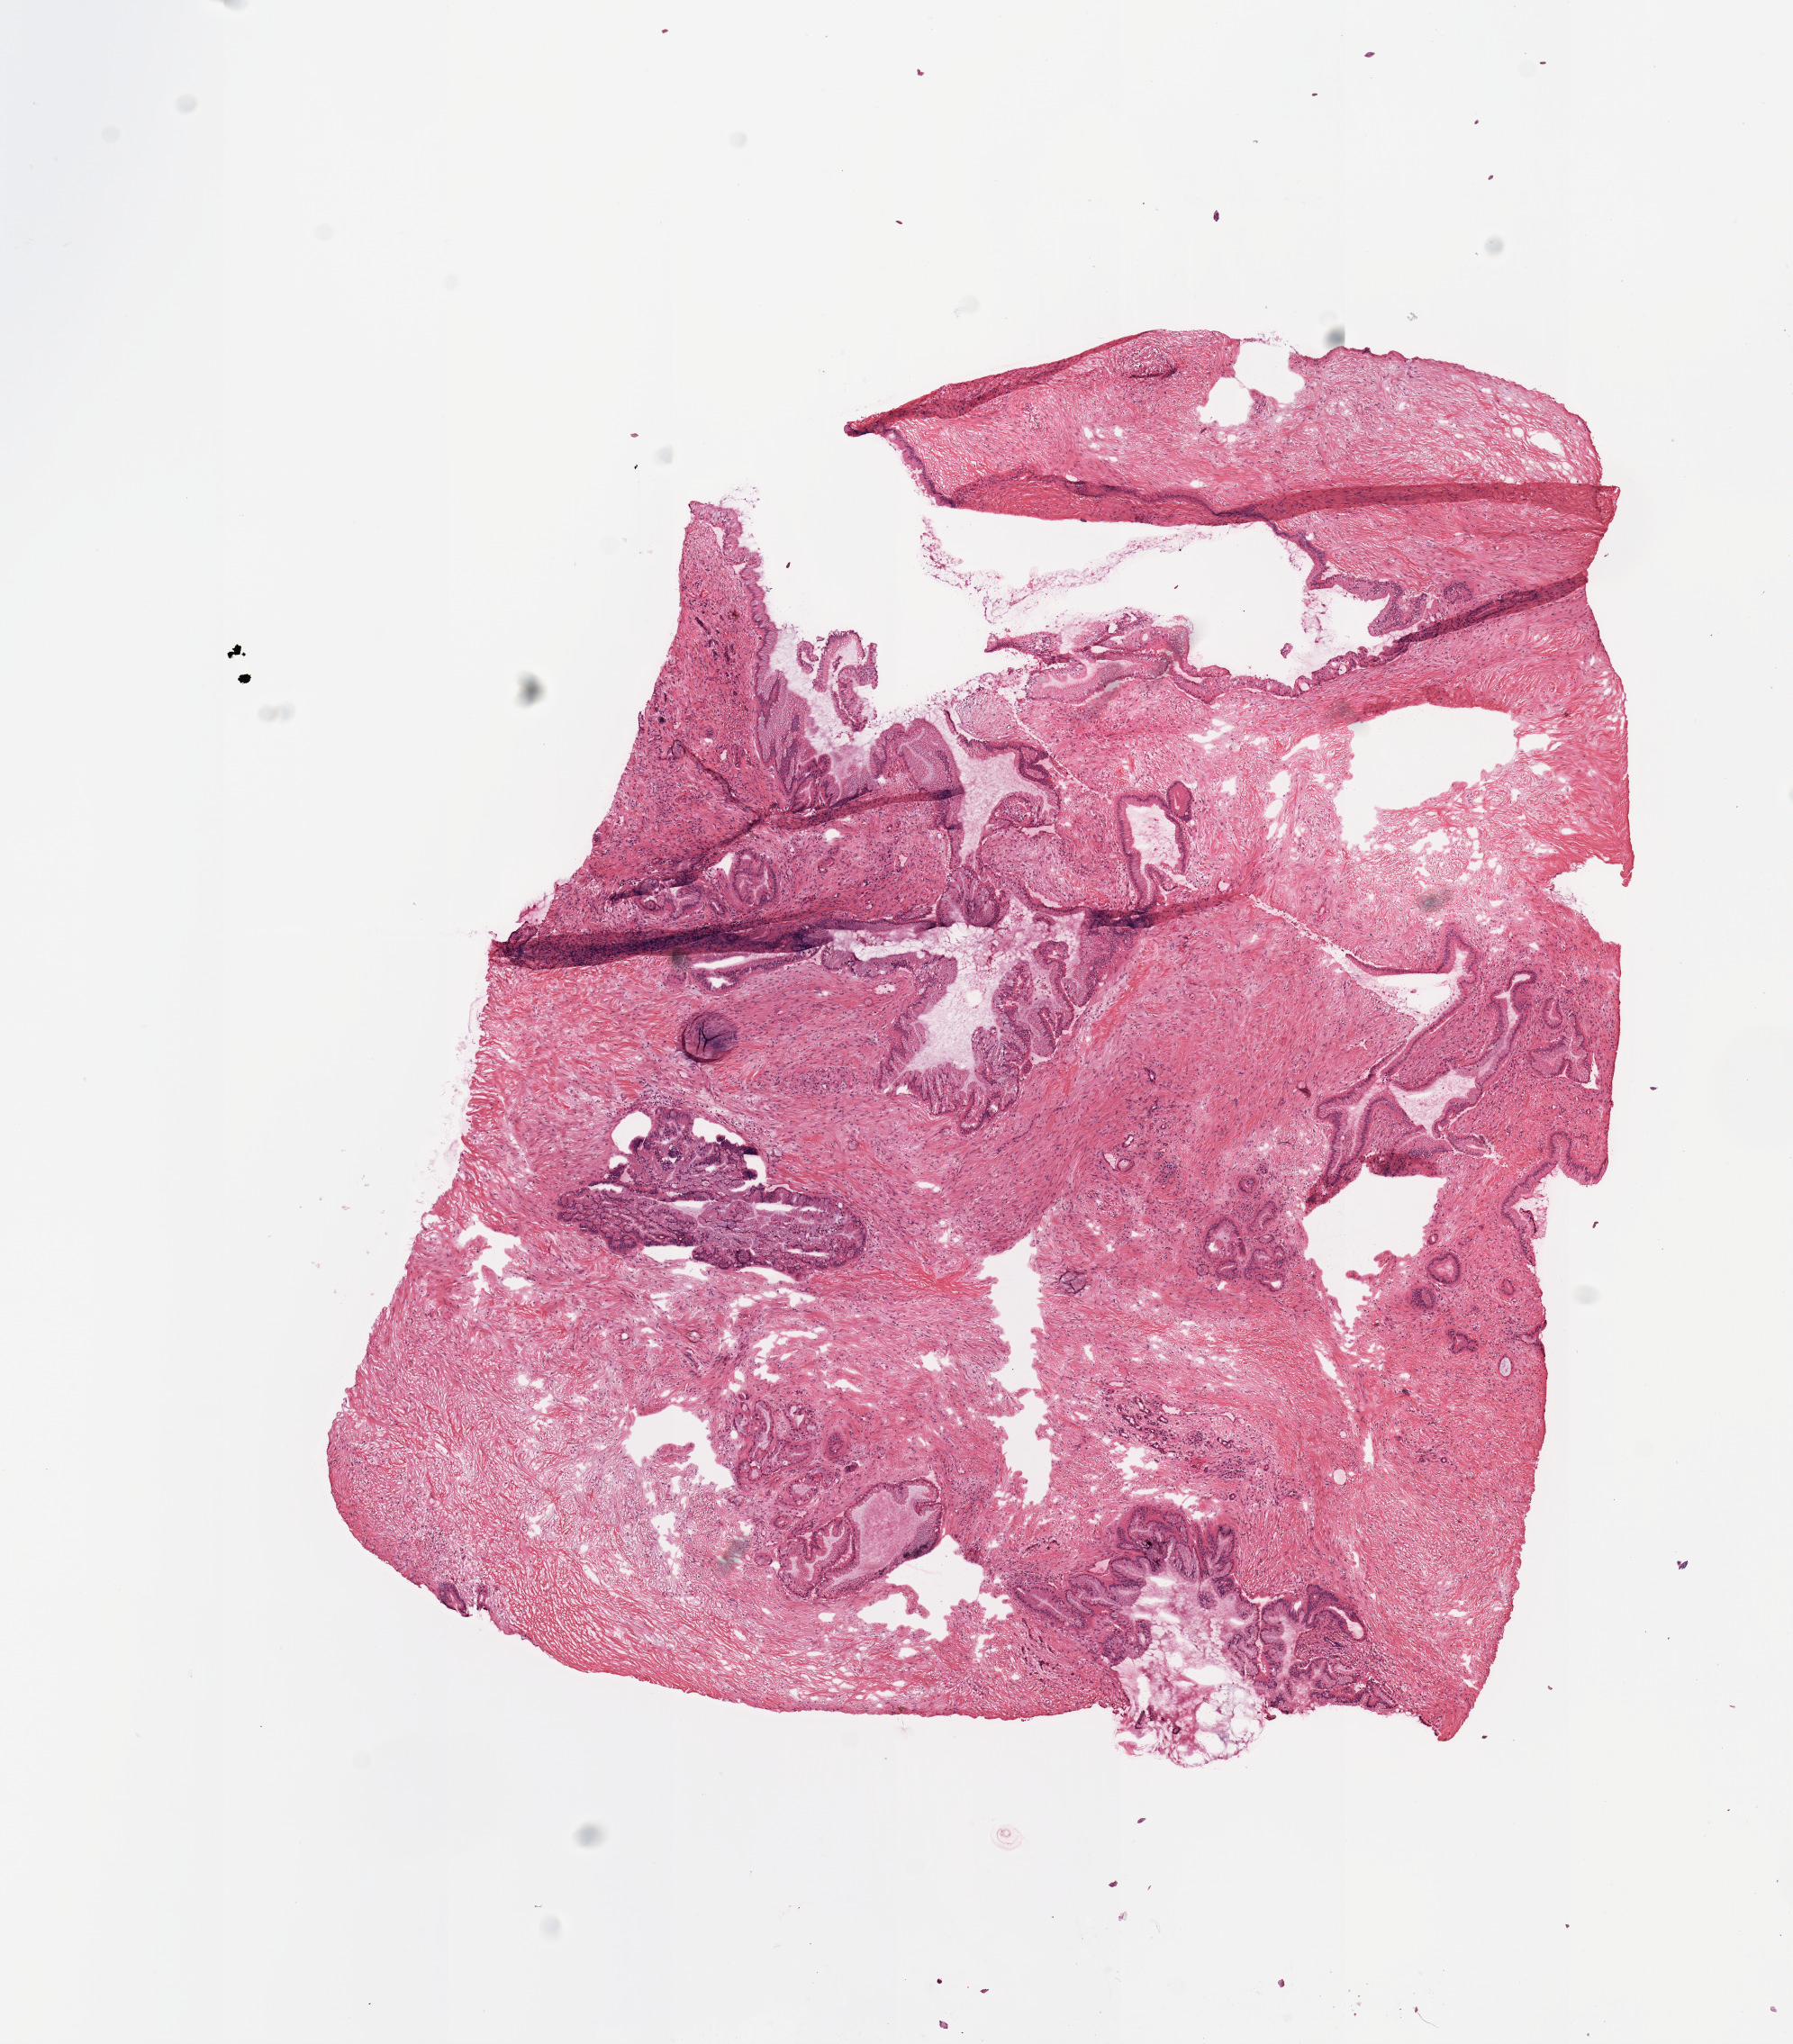
Hematoxylin and eosin (H&E) stained whole-slide image, low-resolution overview of the scanned area, about 7.9 x 9.0 mm (acquisition: 20x scan), tumour tissue sample, pancreas. Patient: male, age 75 years.
Patient diagnosis (cohort enrolment): ductal adenocarcinoma (pancreas).